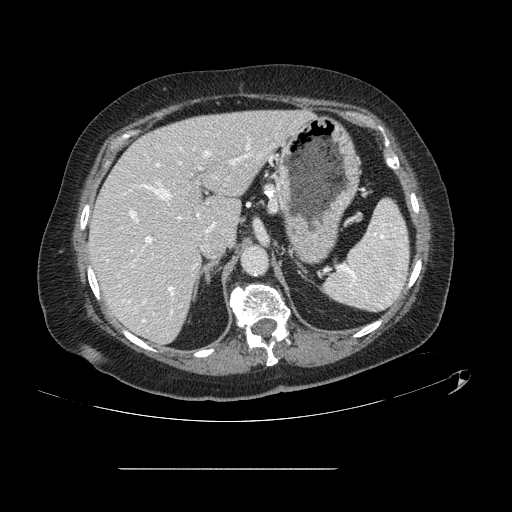
Contrast-enhanced abdominal CT, one axial slice; slice 87 of 148 in the series (ordered by position); 120 kVp; soft-tissue window (W 400 / L 40 HU); 2.5 mm slice thickness; 512 × 512 image matrix, field of view 439 × 439 mm. Female patient, age 75 years. Case-level facts recorded for this patient, not image findings: diagnosis: colorectal cancer liver metastases, imaged before liver resection; multiple liver metastases: no.
Structures marked on this image (outlined manually by an expert reader):
- hepatic veins: box from (x=129, y=152) to (x=209, y=322) px
- liver: (x=90, y=111)–(x=308, y=343)
- planned liver remnant (the part of the liver to remain after resection): (x=90, y=111)–(x=308, y=343)
- portal vein (with intrahepatic branches): (x=130, y=137)–(x=262, y=294)